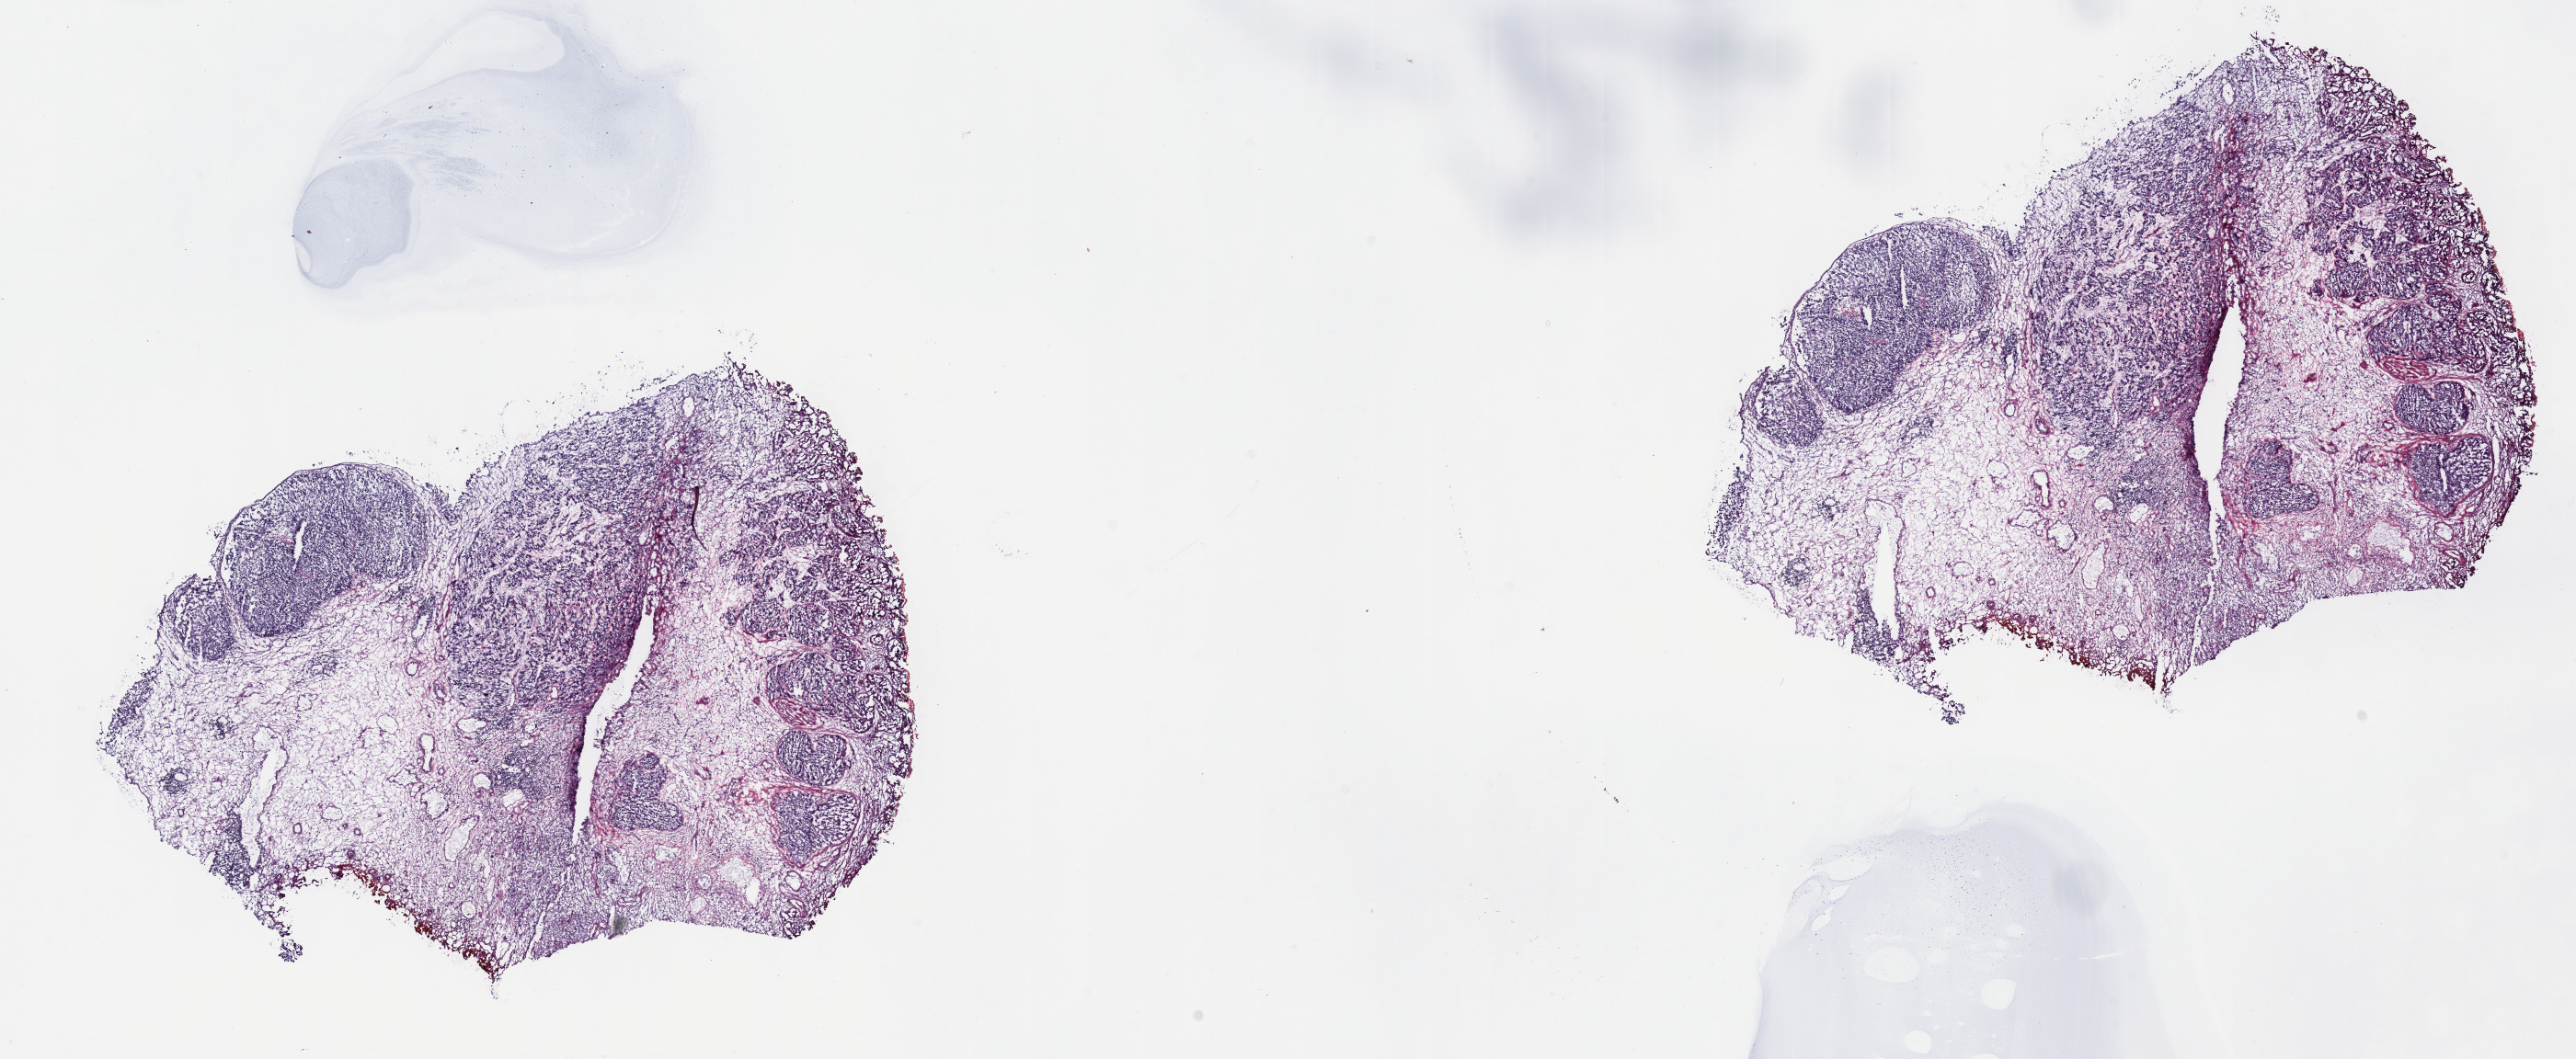
Digitized H&E-stained tissue section (whole slide) — shown as a low-resolution overview of the whole scanned area (about 22.7 x 9.3 mm, slide scanned at 40x), frozen section, sample: primary tumour, bladder. Male patient; age at initial diagnosis 60 years. Histologic grade: high grade. Pathologist review of this section (percent, as recorded): tumour cells 60%, tumour nuclei 65%, normal cells 40%, stromal cells 0%, necrosis 0%. Inflammatory infiltration, as recorded: lymphocyte infiltration 3%, monocyte infiltration 0%, neutrophil infiltration 0%.
* AJCC pathologic stage: IV
* pathologic diagnosis: Transitional cell carcinoma